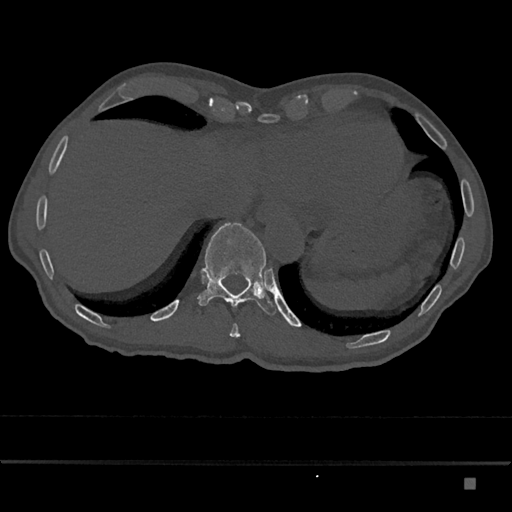
CT including the spine, one axial slice. Position 687 of 797 along the scan axis. Bone window (W 1800 / L 400 HU). 0.5 mm slice thickness. 512 × 512 image matrix, field of view 390 × 390 mm. Male patient, age 72 years. From the clinical record (not read from this slice): primary cancer: prostate.
Annotated regions visible in this slice (semi-automatic segmentation, software-assisted and operator-edited):
- T10 vertebra: box from (x=230, y=323) to (x=240, y=337) px
- T11 vertebra: (x=198, y=223)–(x=276, y=315)